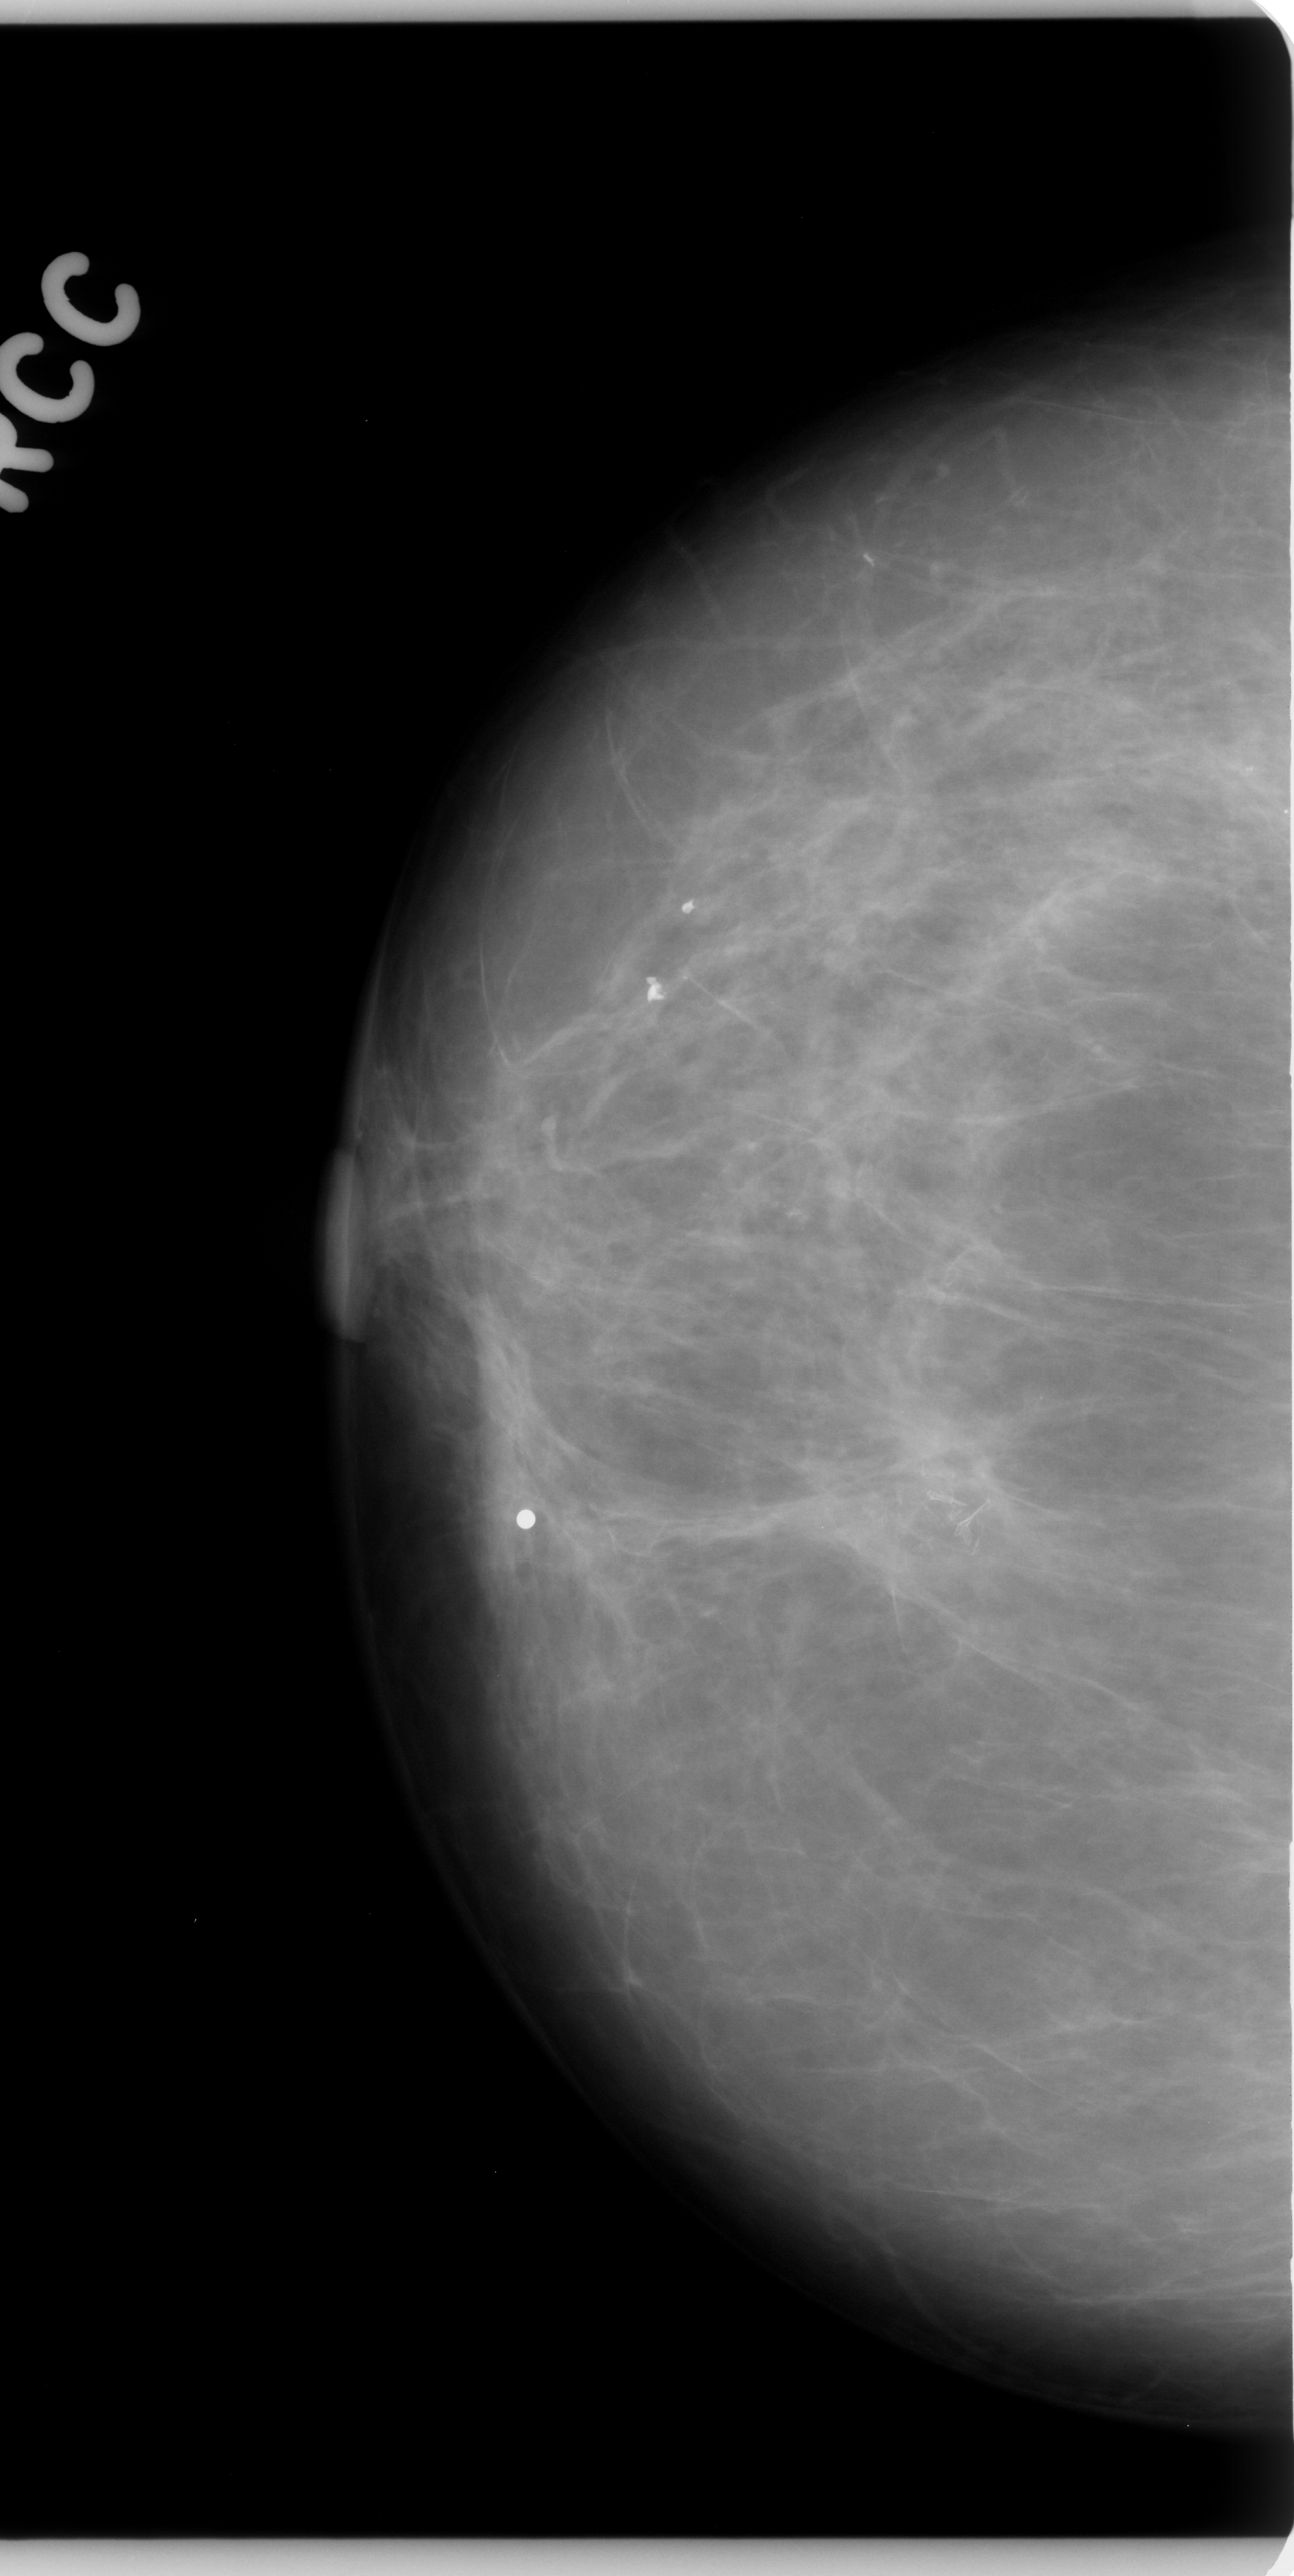
Mammogram (digitized film); right breast; CC view; breast composition: scattered fibroglandular densities (BI-RADS density category 2 of 4); 1294 × 2576 image matrix.
Expert-marked regions of interest on this film, with their recorded descriptors:
- calcifications, morphology fine linear branching, distribution clustered; BI-RADS assessment category 4; pathology result (as recorded, not read from the image): benign: box from (x=841, y=1389) to (x=1066, y=1554) px